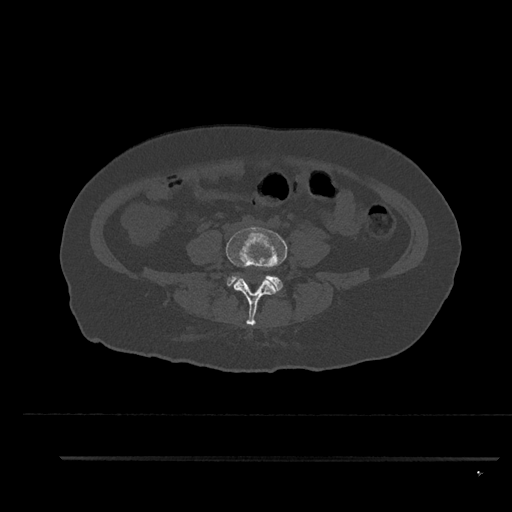
CT including the spine, one axial slice. Slice 1 of 797 in the series (ordered by position). 120 kVp. Bone window (W 1800 / L 400 HU). 0.5 mm slice thickness. 512 × 512 image matrix, field of view 408 × 408 mm. Patient: female, 44 years. From the clinical record (not read from this slice): primary cancer: renal; vertebrae with lytic lesions (as recorded): L1.
Annotated regions visible in this slice (semi-automatically segmented with operator editing):
- L4 vertebra: bounding box <226,227,287,326> (left, top, right, bottom; pixels)